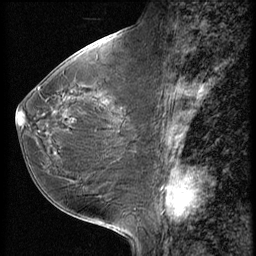
Breast MRI (dynamic contrast-enhanced), one sagittal slice. Position 25 of 56 along the scan axis. 3 images stored at this slice position (order not interpretable as contrast timing). 1.5 T. TE 4.2 ms, TR 9 ms. 2.5 mm slice thickness. 256 × 256 image matrix, field of view 180 × 180 mm. Female patient, age 49 years. From the clinical record (not read from this slice): setting: breast cancer imaged before/during neoadjuvant chemotherapy; receptor status: HER2-positive.
Outlined on this slice (semi-automatically segmented with operator editing):
- analysis volume of interest (the breast-tissue region the enhancement analysis was run in; not a lesion): box from (x=17, y=74) to (x=148, y=198) px
- tumour enhancement mask (voxels above the 140 % enhancement threshold inside the analysis volume of interest): (x=17, y=112)–(x=66, y=126)